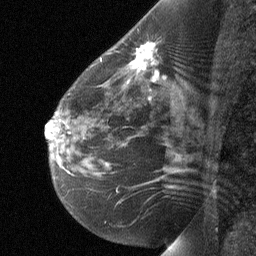
Breast MRI (dynamic contrast-enhanced), one sagittal slice. Position 37 of 64 along the scan axis. Dynamic contrast-enhanced study with each time point stored as its own series, time point 2 of 3 at this slice position (early post-contrast, ordered by acquisition time). 1.5 T. TE 4.8 ms, TR 27 ms. 2 mm slice thickness. 256 × 256 image matrix. Female patient, age 51 years. From the clinical record (not read from this slice): setting: breast cancer imaged before/during neoadjuvant chemotherapy; receptor status: HR-positive, HER2-negative.
Structures marked on this image (semi-automatically segmented with operator editing):
- analysis volume of interest (the breast-tissue region the enhancement analysis was run in; not a lesion): bounding box <81,35,179,103> (left, top, right, bottom; pixels)
- tumour enhancement mask (voxels above the 90 % enhancement threshold inside the analysis volume of interest): <133,43,154,80>